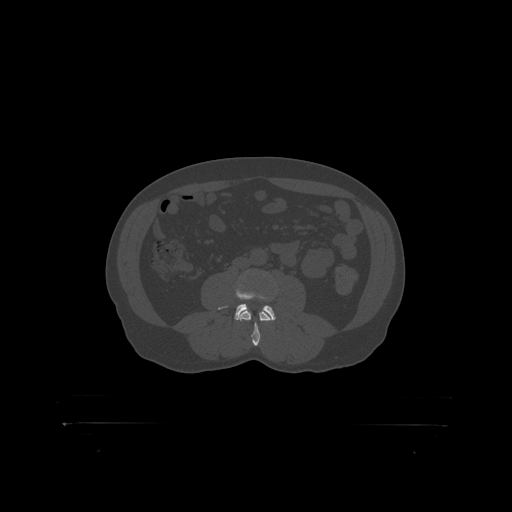
CT including the spine, one axial slice. Slice 251 of 399 in the series (ordered by position). Reconstruction kernel STANDARD. 120 kVp. Bone window (W 1800 / L 400 HU). 1.25 mm slice thickness. 512 × 512 image matrix. Male patient, age 46 years. From the clinical record (not read from this slice): primary cancer: skin.
Structures marked on this image (semi-automatically segmented with operator editing):
- L3 vertebra: box from (x=240, y=309) to (x=269, y=319) px
- L4 vertebra: (x=221, y=289)–(x=275, y=317)